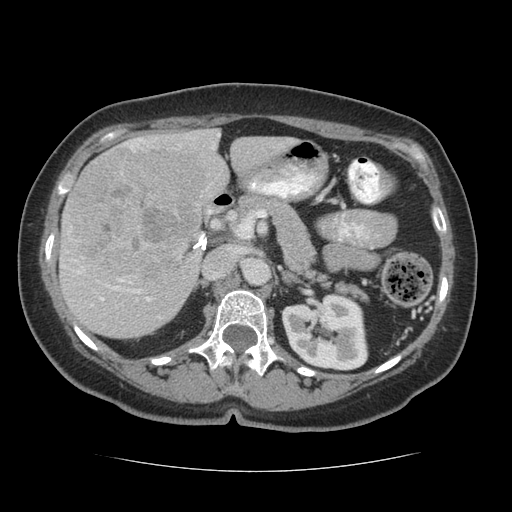
Contrast-enhanced abdominal CT (liver protocol), one axial slice; slice 31 of 75 in the series (ordered by position); soft-tissue window (W 400 / L 40 HU); 2.5 mm slice thickness; 512 × 512 image matrix, field of view 360 × 360 mm. From the clinical record (not read from this slice): diagnosis: hepatocellular carcinoma (patient treated with transarterial chemoembolisation; whether this scan precedes or follows treatment is not stated here); TNM stage (as recorded): Stage-I; Child-Pugh class: A.
Structures marked on this image (semi-automatically segmented with operator editing):
- liver parenchyma outside the tumour (the mass and vessels are separate outlines, so this box may not span the whole liver): bounding box [x1, y1, x2, y2] px = [58, 128, 295, 338]
- mass: [67, 148, 207, 286]
- liver vessels: [61, 134, 220, 318]